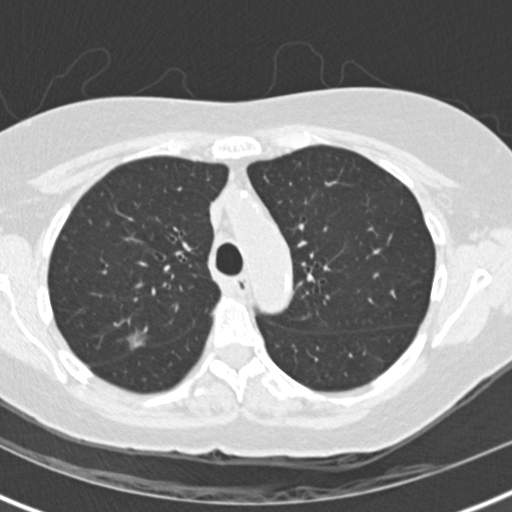
Low-dose screening chest CT, one axial slice. Slice 101 of 147 in the series (ordered by position). Lung window (W 1500 / L -600 HU). 2 mm slice thickness. 512 × 512 image matrix, field of view 300 × 300 mm.
Annotated regions visible in this slice (expert manual segmentation):
- lesion 1 (tumor, upper lobe of right lung): bounding box [x1, y1, x2, y2] px = [127, 331, 145, 350]